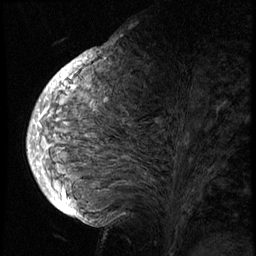
Breast MRI (dynamic contrast-enhanced), one sagittal slice. Slice 33 of 74 in the series (ordered by position). 3 images stored at this slice position (order not interpretable as contrast timing). 1.5 T. TE 4.2 ms, TR 8.9 ms. 2.5 mm slice thickness. 256 × 256 image matrix. Female patient, age 57 years. Case-level facts recorded for this patient, not image findings: setting: breast cancer imaged before/during neoadjuvant chemotherapy; receptor status: HER2-positive.
Structures marked on this image (semi-automatically segmented with operator editing):
- analysis volume of interest (the breast-tissue region the enhancement analysis was run in; not a lesion): bounding box (x1, y1, x2, y2) in pixels: (40, 62, 237, 175)
- tumour enhancement mask (voxels above the 140 % enhancement threshold inside the analysis volume of interest): (40, 64, 96, 174)